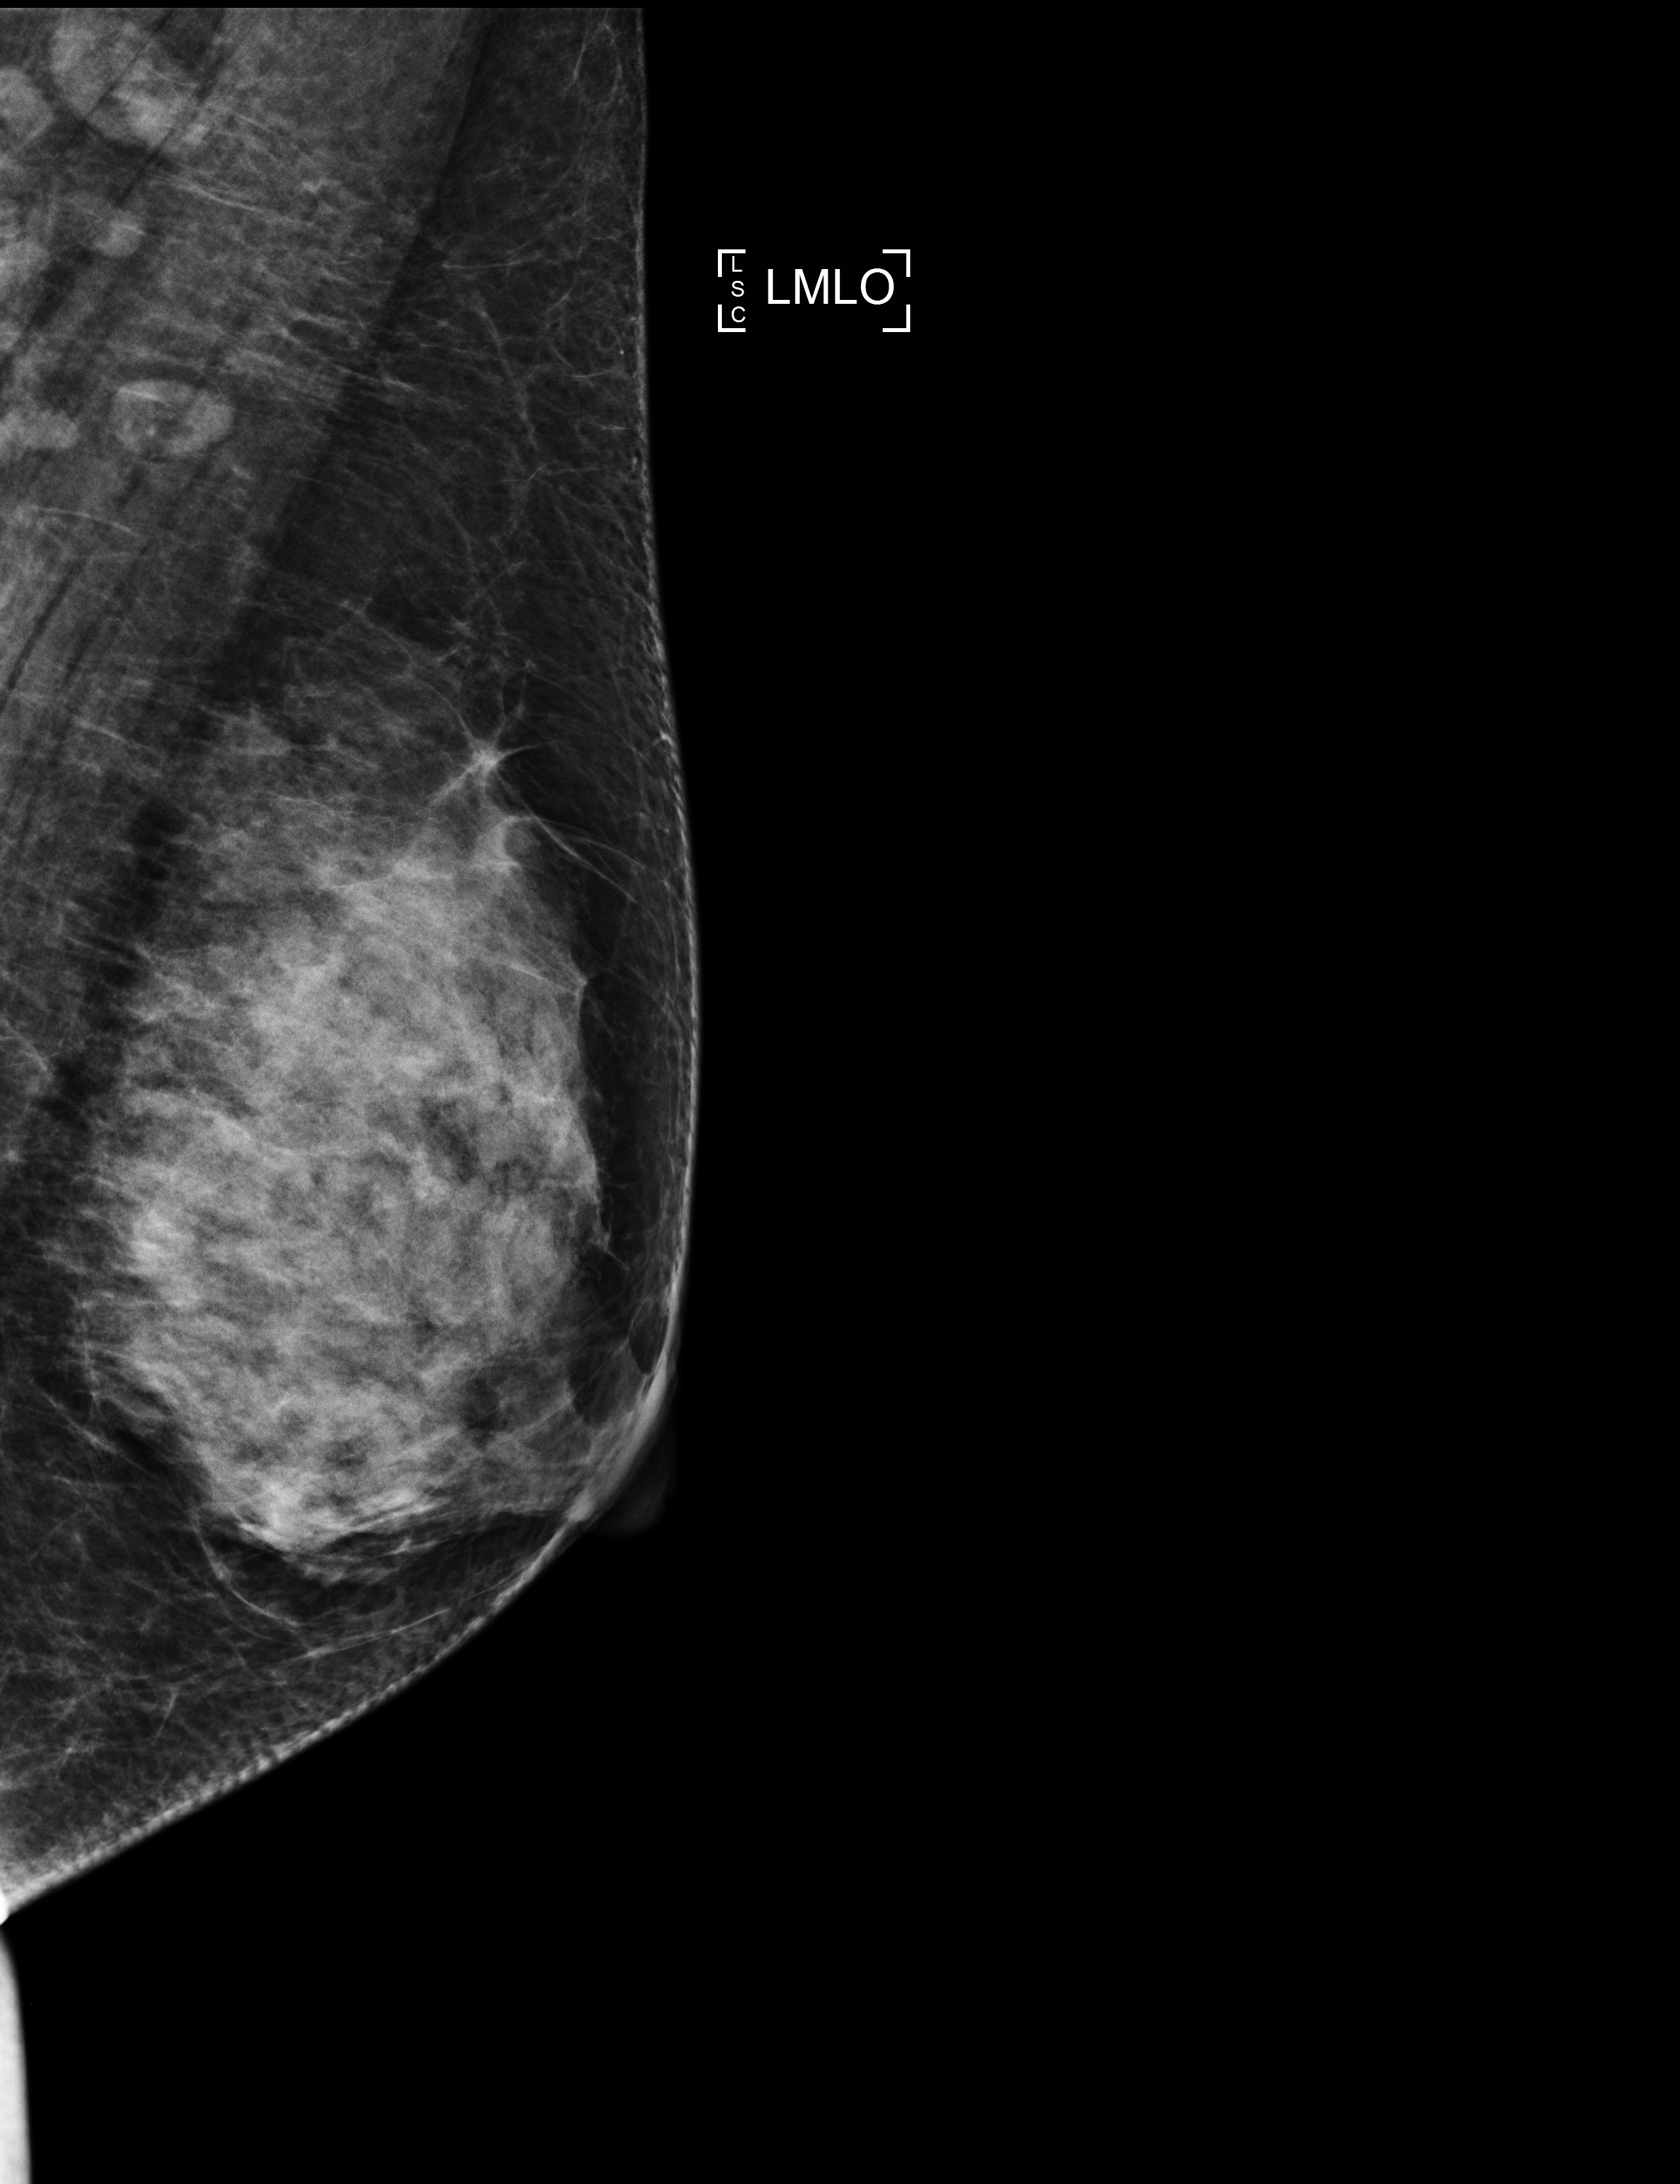
Screening examination; system: Selenia Dimensions. Female patient, age 51 years.
Image type: full-field digital mammogram. Breast: left. Projection: MLO view.